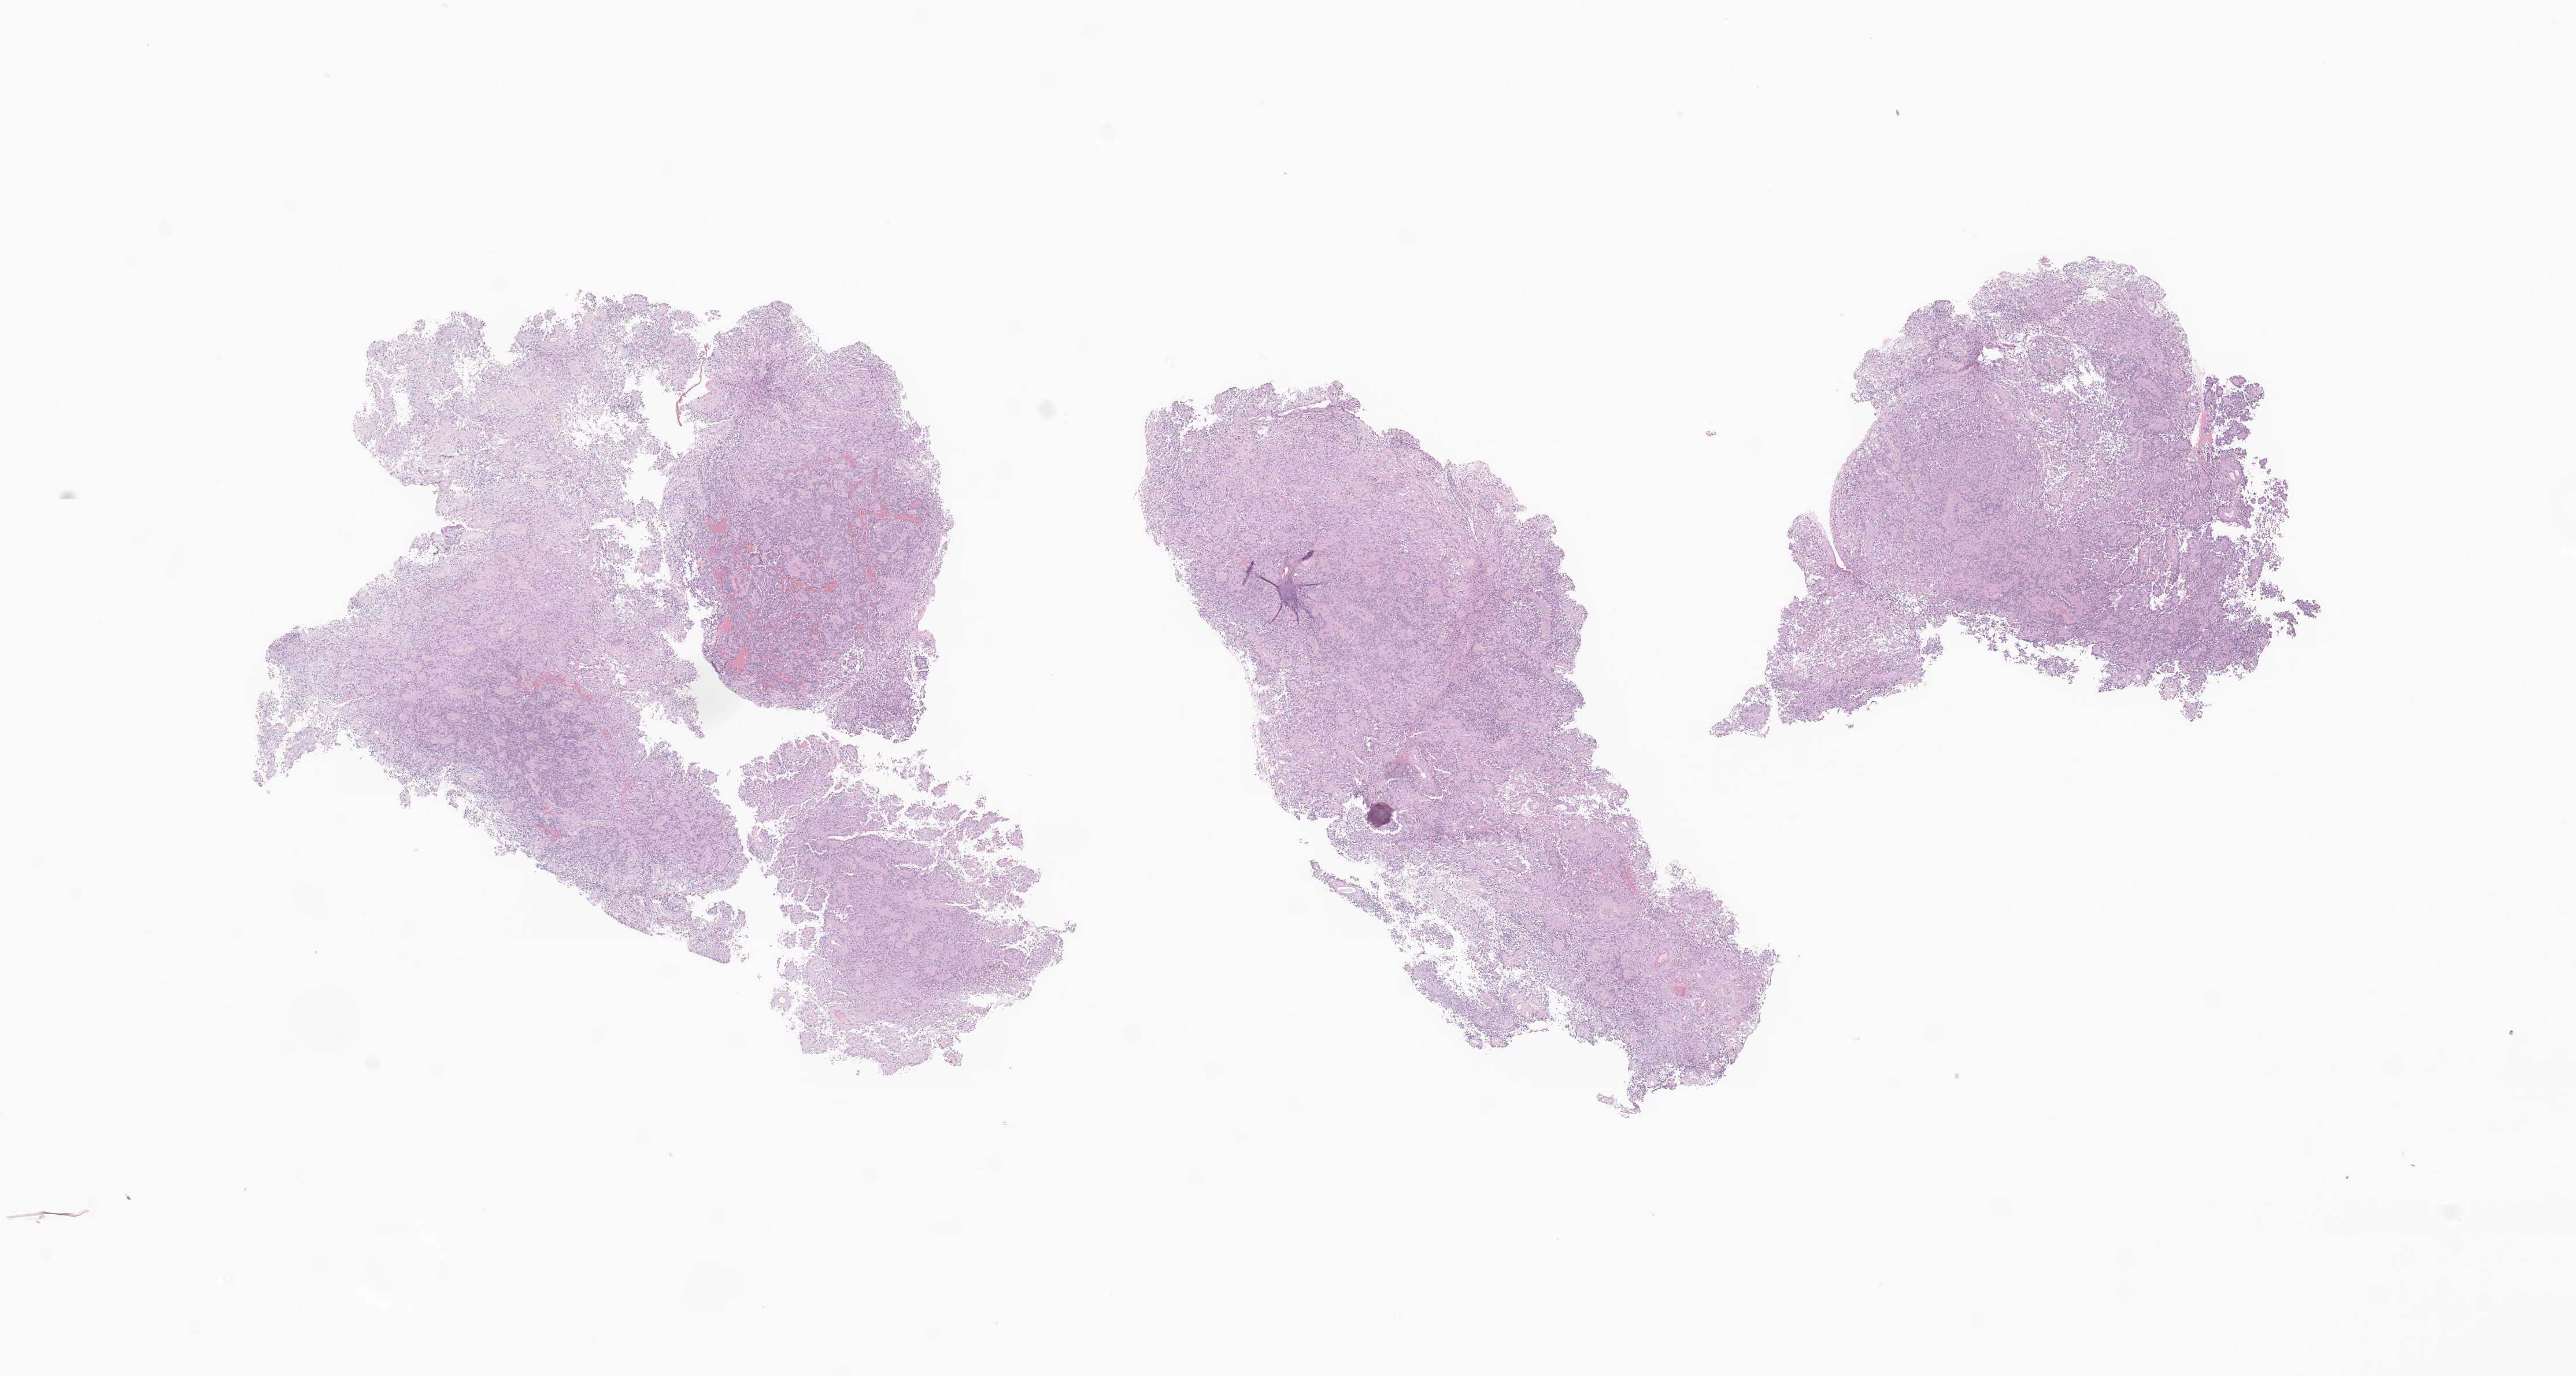
Digitized haematoxylin and eosin-stained section of tumor tissue from the brain, shown as a low-resolution overview of the whole scanned area (about 18.8 x 10.0 mm). Formalin-fixed, paraffin-embedded (FFPE) tissue. Female patient, age 200 months (16 years 8 months).
Recorded diagnosis: Ependymoma, NOS.